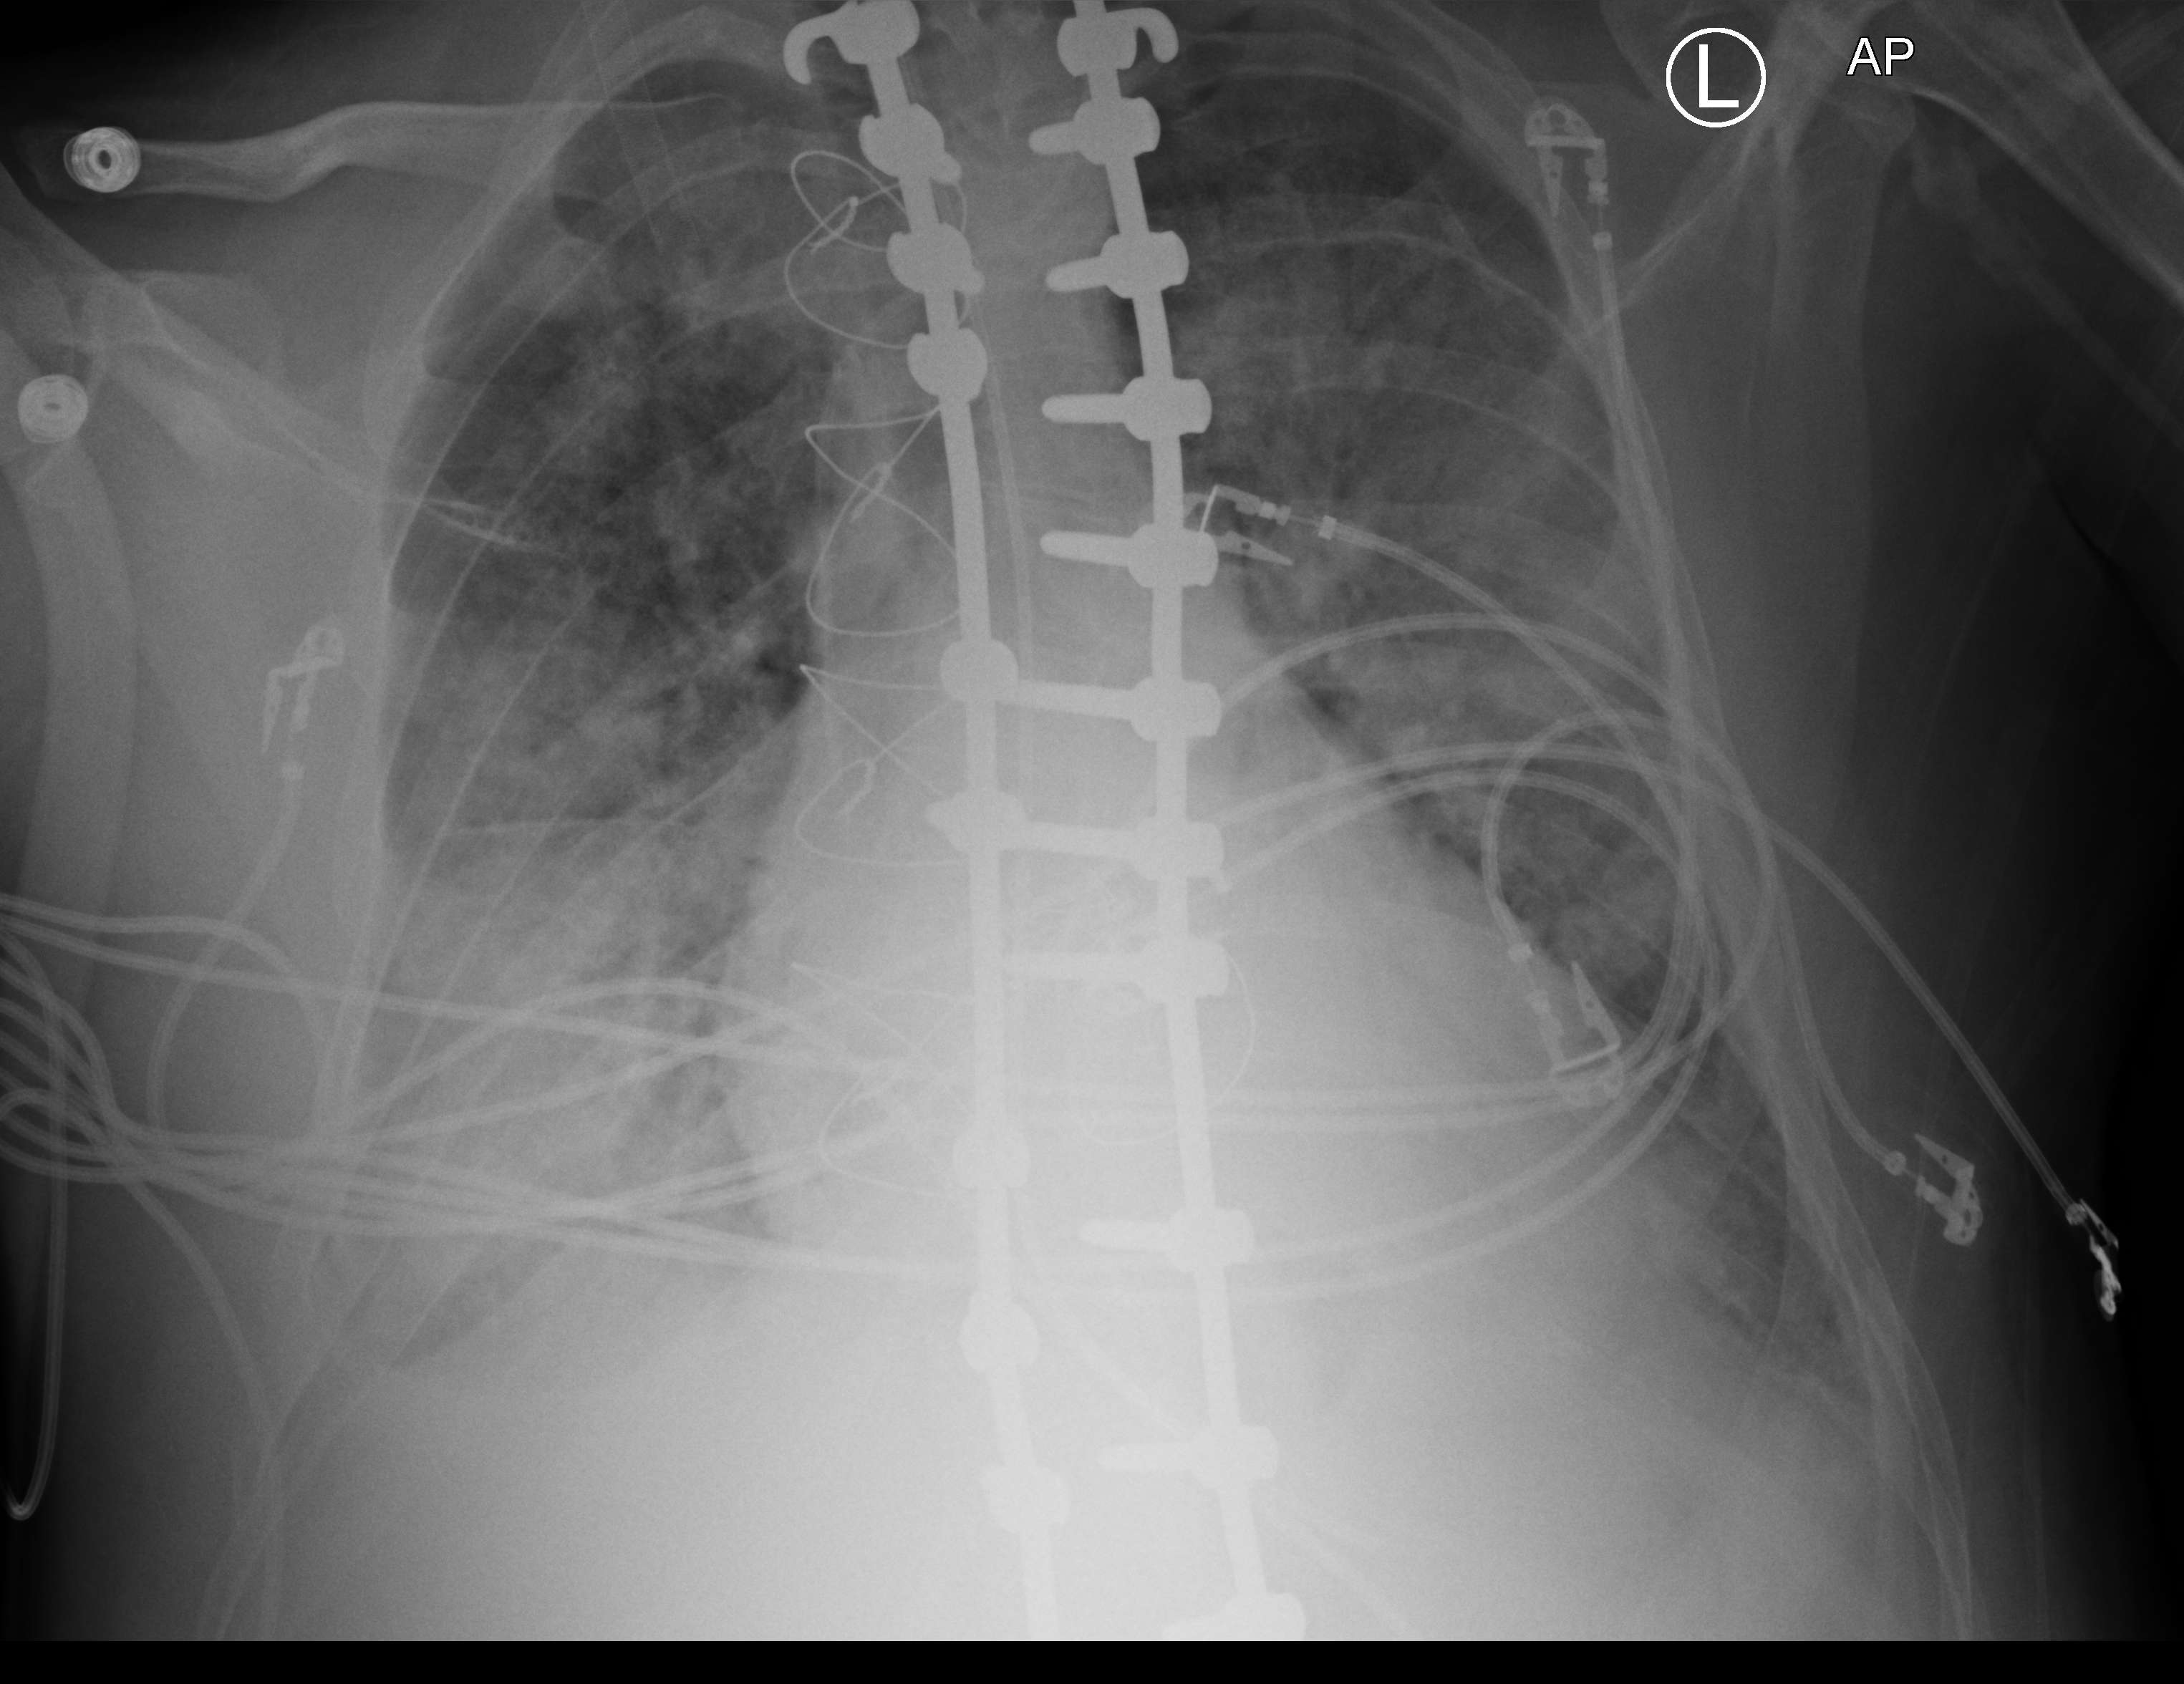
Chest X-ray (portable). Patient hospitalised with COVID-19, aged 18–59 years.
Hospital-stay facts (about this admission, not read from this image; timing relative to this image not recorded):
- mechanically ventilated during this hospital stay: yes
- admitted to intensive care during this hospital stay: yes